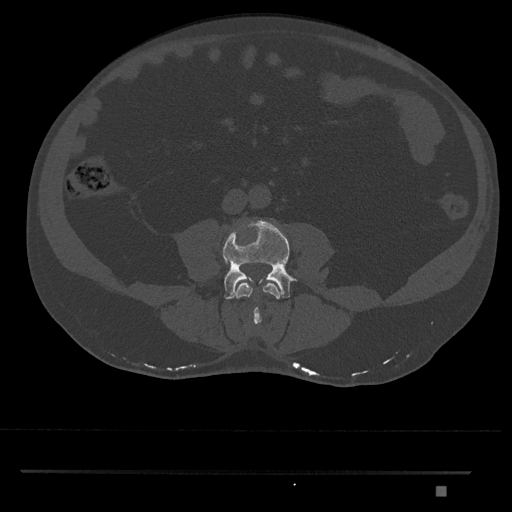
CT including the spine, one axial slice; slice 639 of 1134 in the series (ordered by position); bone window (W 1800 / L 400 HU); 512 × 512 image matrix, field of view 429 × 429 mm. Patient: male, 65 years. From the clinical record (not read from this slice): primary cancer: prostate.
Structures marked on this image (semi-automatically segmented with operator editing):
- L3 vertebra: bounding box (x1, y1, x2, y2) in pixels: (236, 282, 280, 325)
- L4 vertebra: (223, 220, 296, 299)